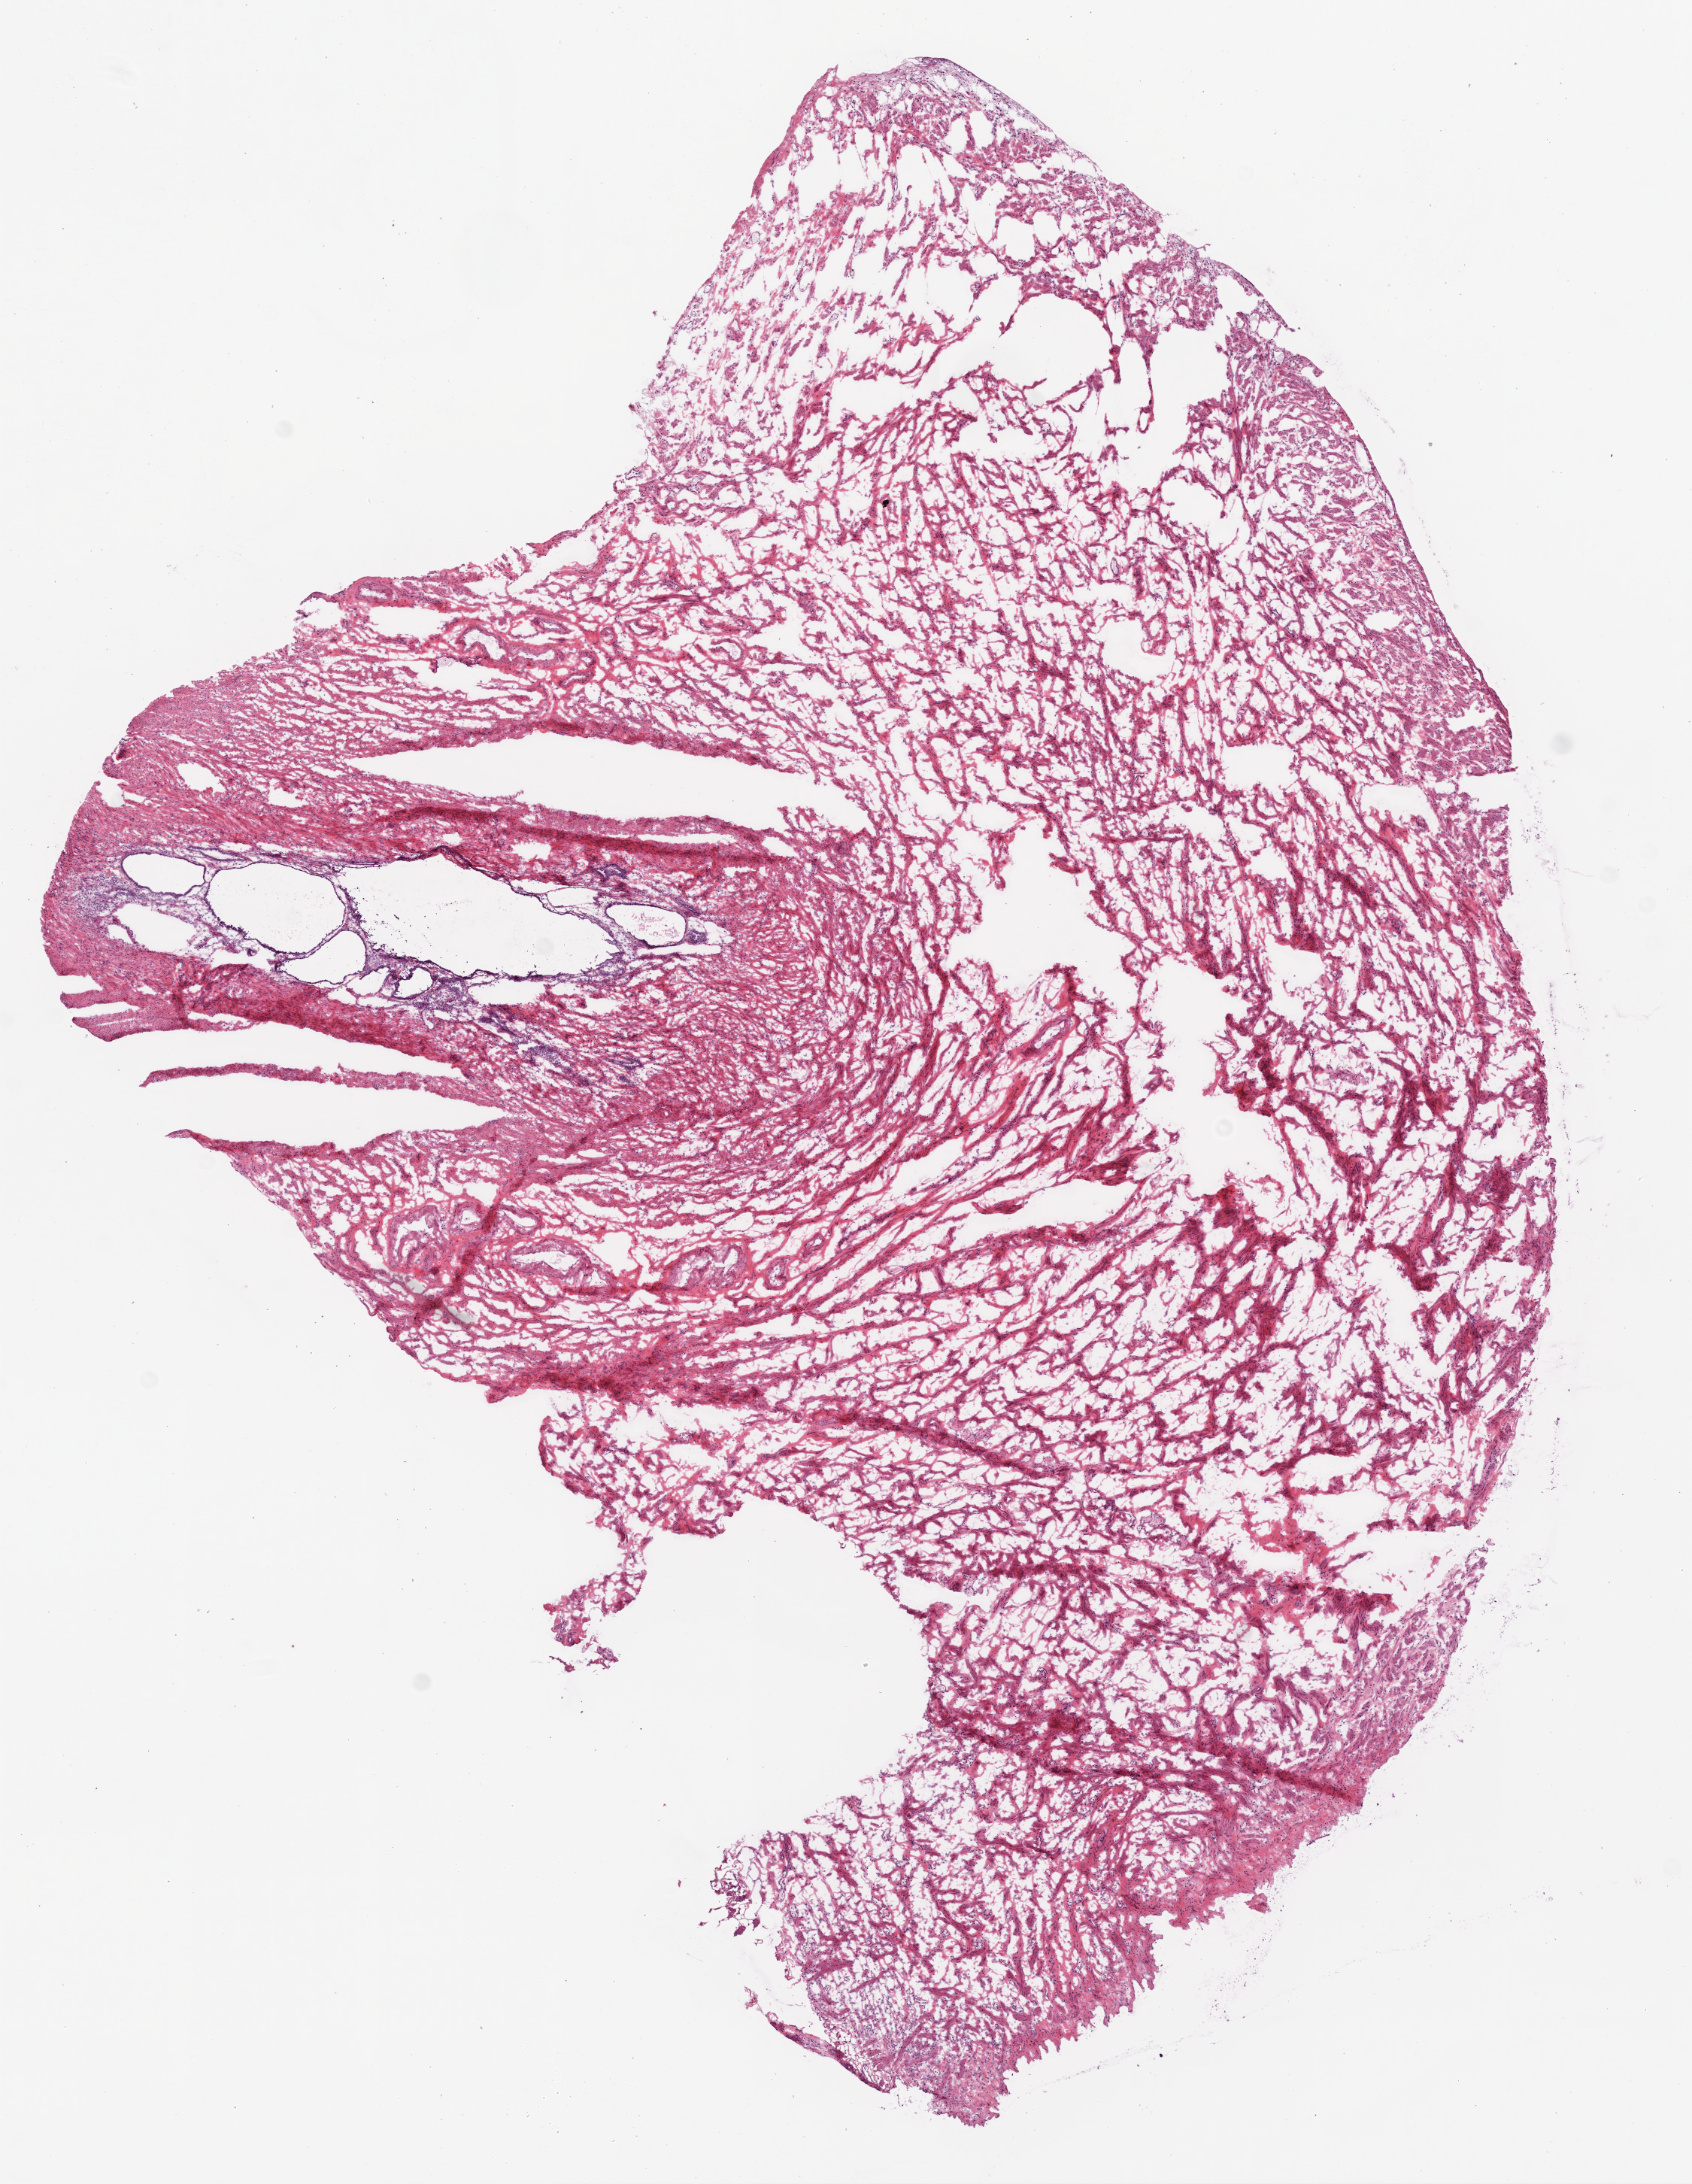
Whole-slide histology image, H&E — a low-resolution overview of the entire scanned area, about 9.0 x 11.7 mm (from a 20x scan), frozen section, ovary, solid tissue normal (non-tumour tissue) sample. Female patient; age at initial diagnosis 60 years.
This section: solid tissue normal (non-tumour) sample from the same patient. Patient diagnosis: Serous cystadenocarcinoma, NOS.